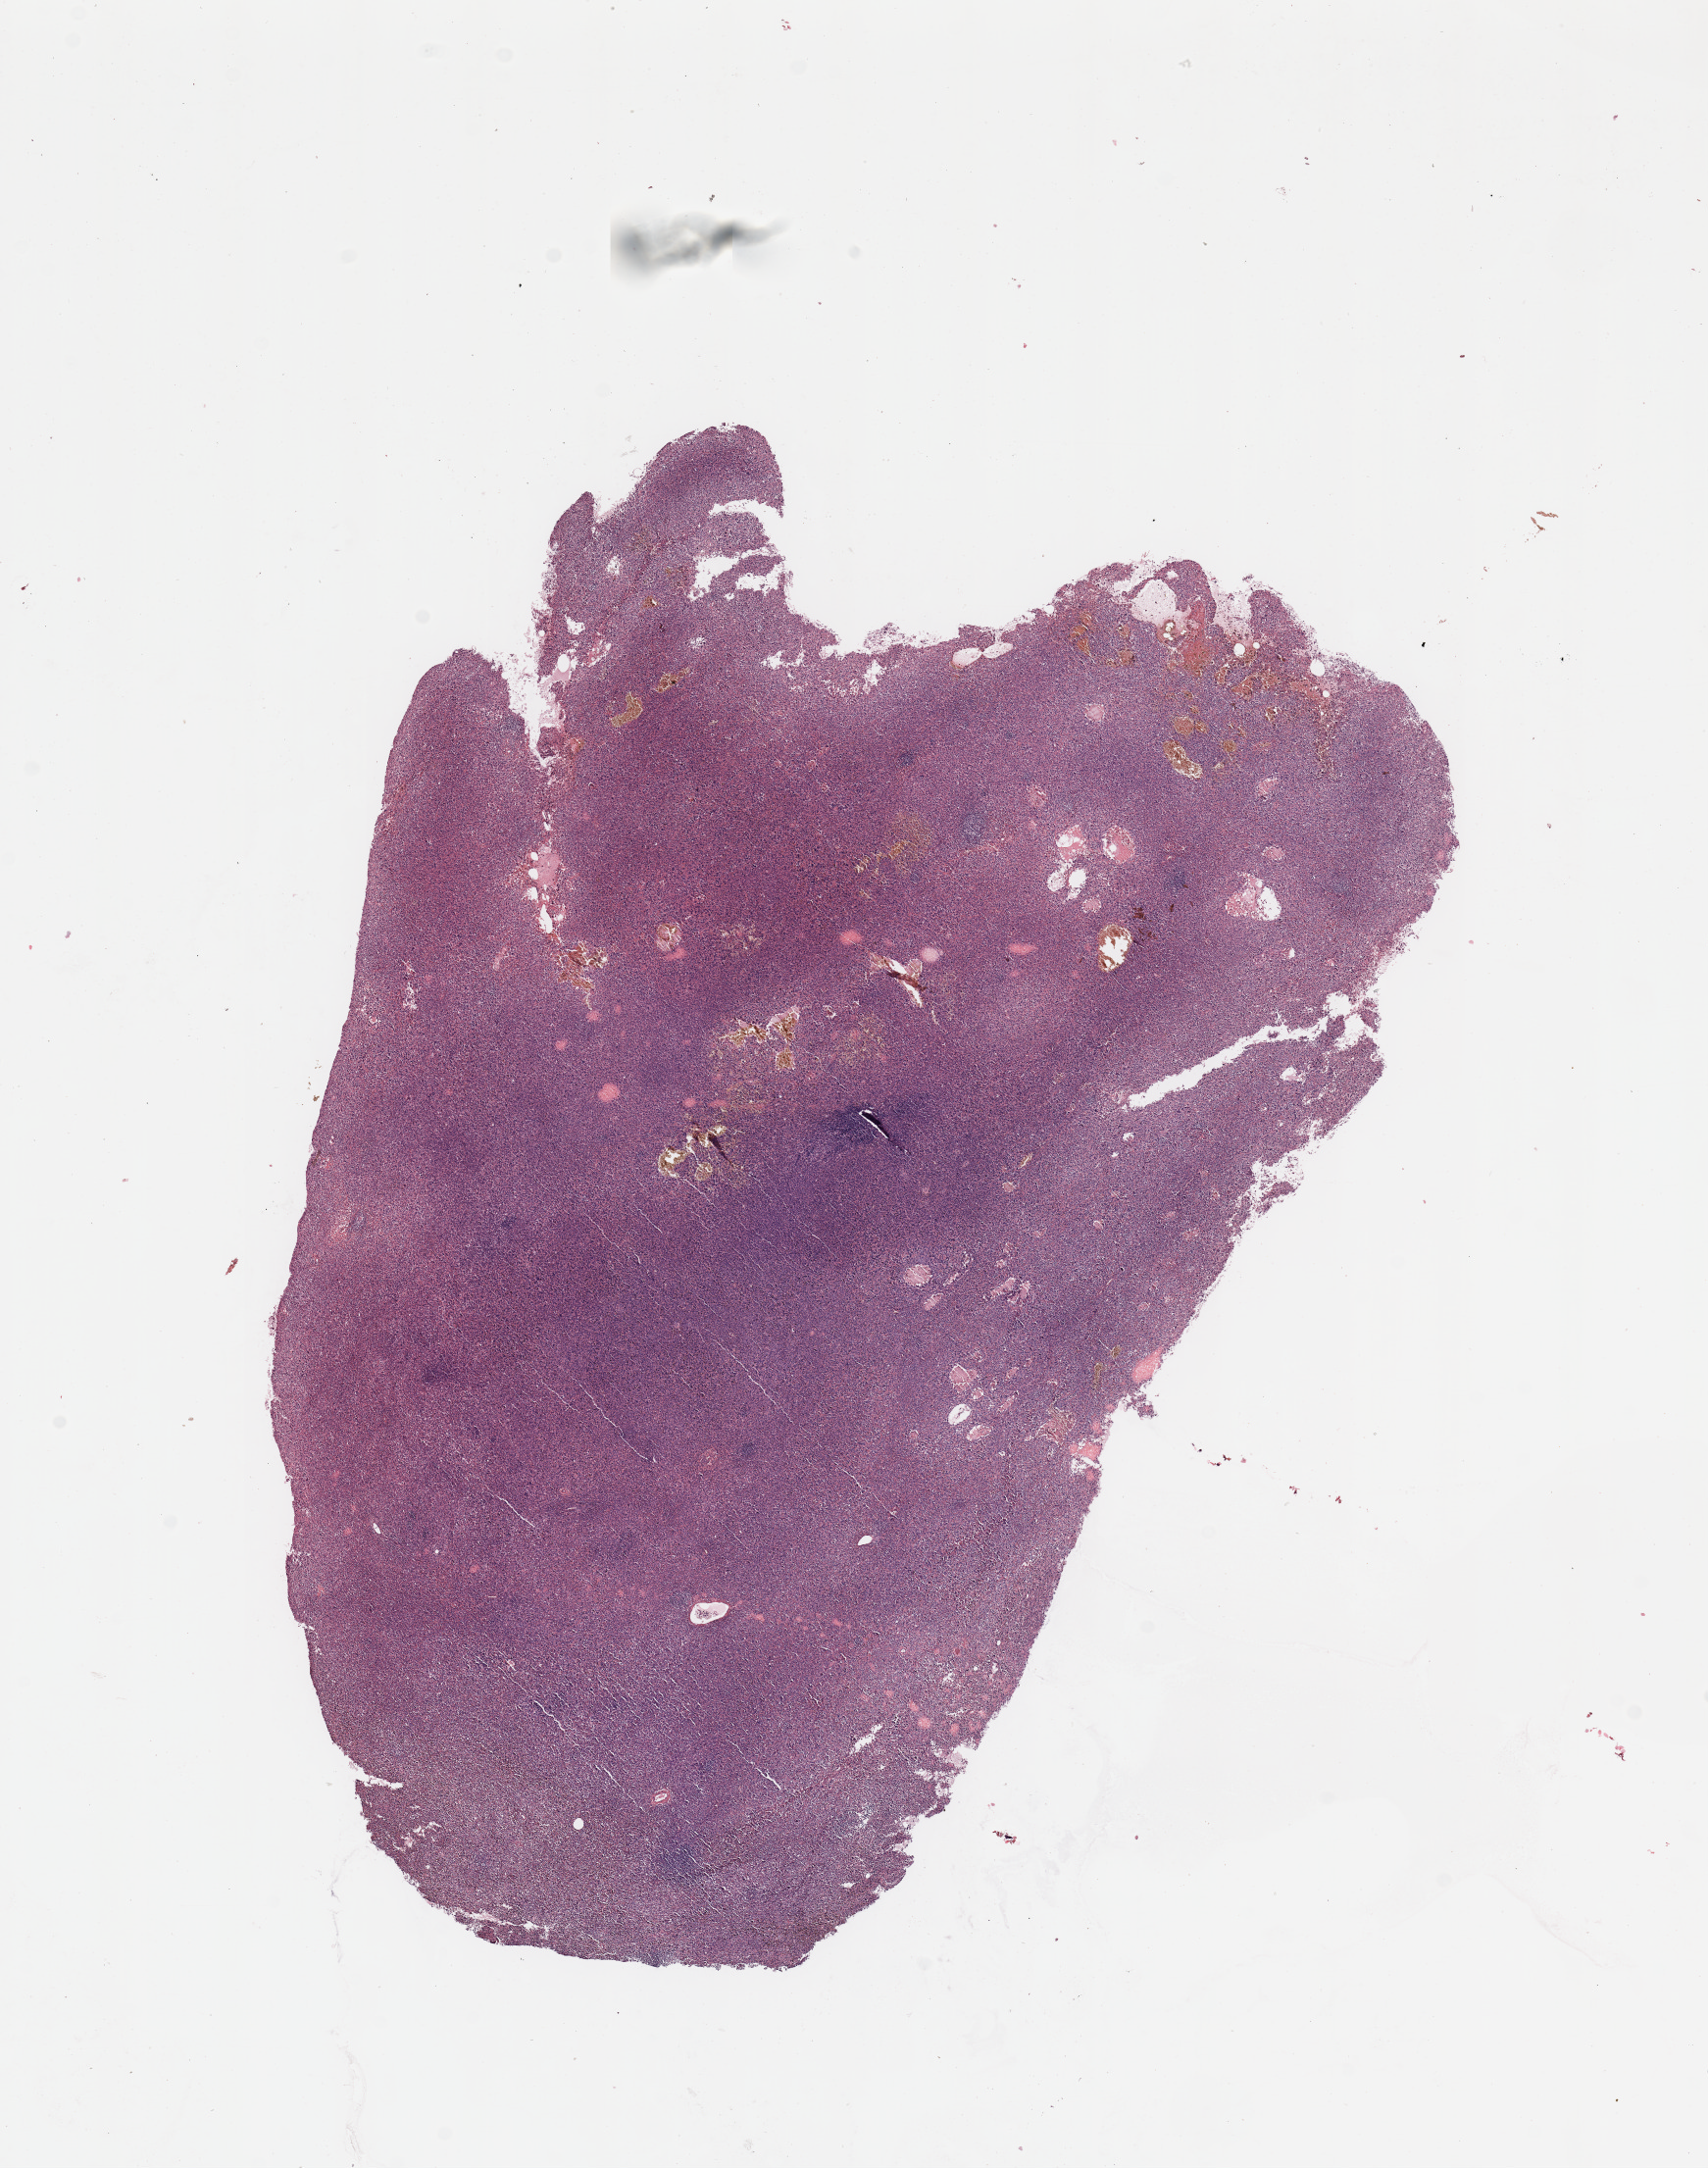
Whole-slide histology image, H&E, whole scanned area (about 13.8 x 17.5 mm, acquisition: 20x scan) shown as a low-resolution overview; tumour tissue sample, sampled site: skin. Patient: male, age 77 years. Composition of this section per pathologist review: tumour nuclei 95%, necrosis 2%.
This section: metastatic tumour tissue. Patient diagnosis: Malignant melanoma, NOS.